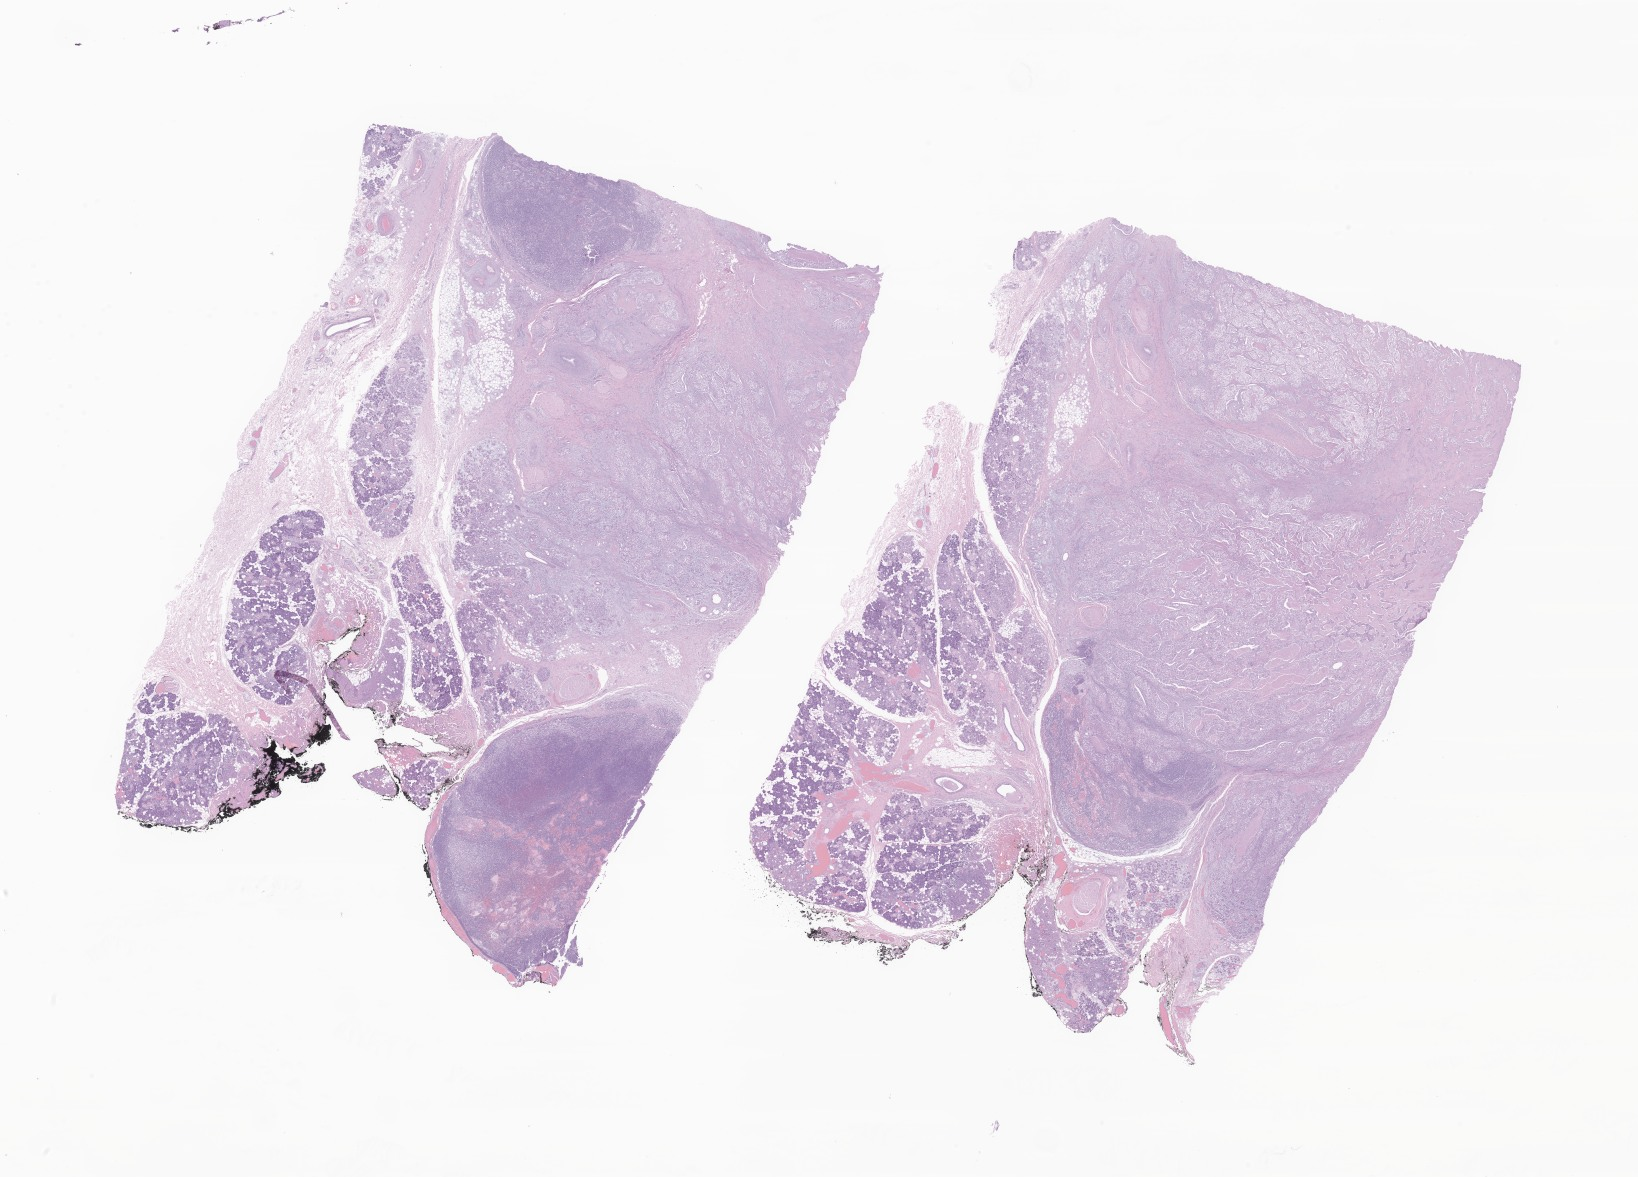
H&E whole-slide image of tumor tissue from the parotid gland, a low-resolution overview of the entire scanned area, about 27.6 x 19.9 mm; formalin-fixed, paraffin-embedded (FFPE) tissue. Patient: female, age 192 months (16 years).
Diagnosis (ICD-O-3 morphology term): Adenoid cystic carcinoma.